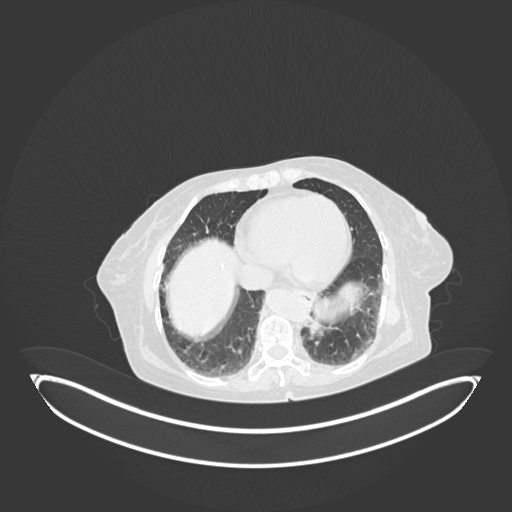
Chest CT, one axial slice. Slice 17 of 189 in the series (ordered by position). Reconstruction kernel B30f. 120 kVp. Lung window (W 1500 / L -600 HU). 1 mm slice thickness. 512 × 512 image matrix, field of view 500 × 500 mm. Patient: female, 82 years. Case-level facts recorded for this patient, not image findings: clinical TNM (as recorded): T1b N0 M1.
Outlined on this slice (bounding box drawn by a radiologist):
- lung tumour (recorded histology: adenocarcinoma): box from (x=303, y=314) to (x=340, y=343) px